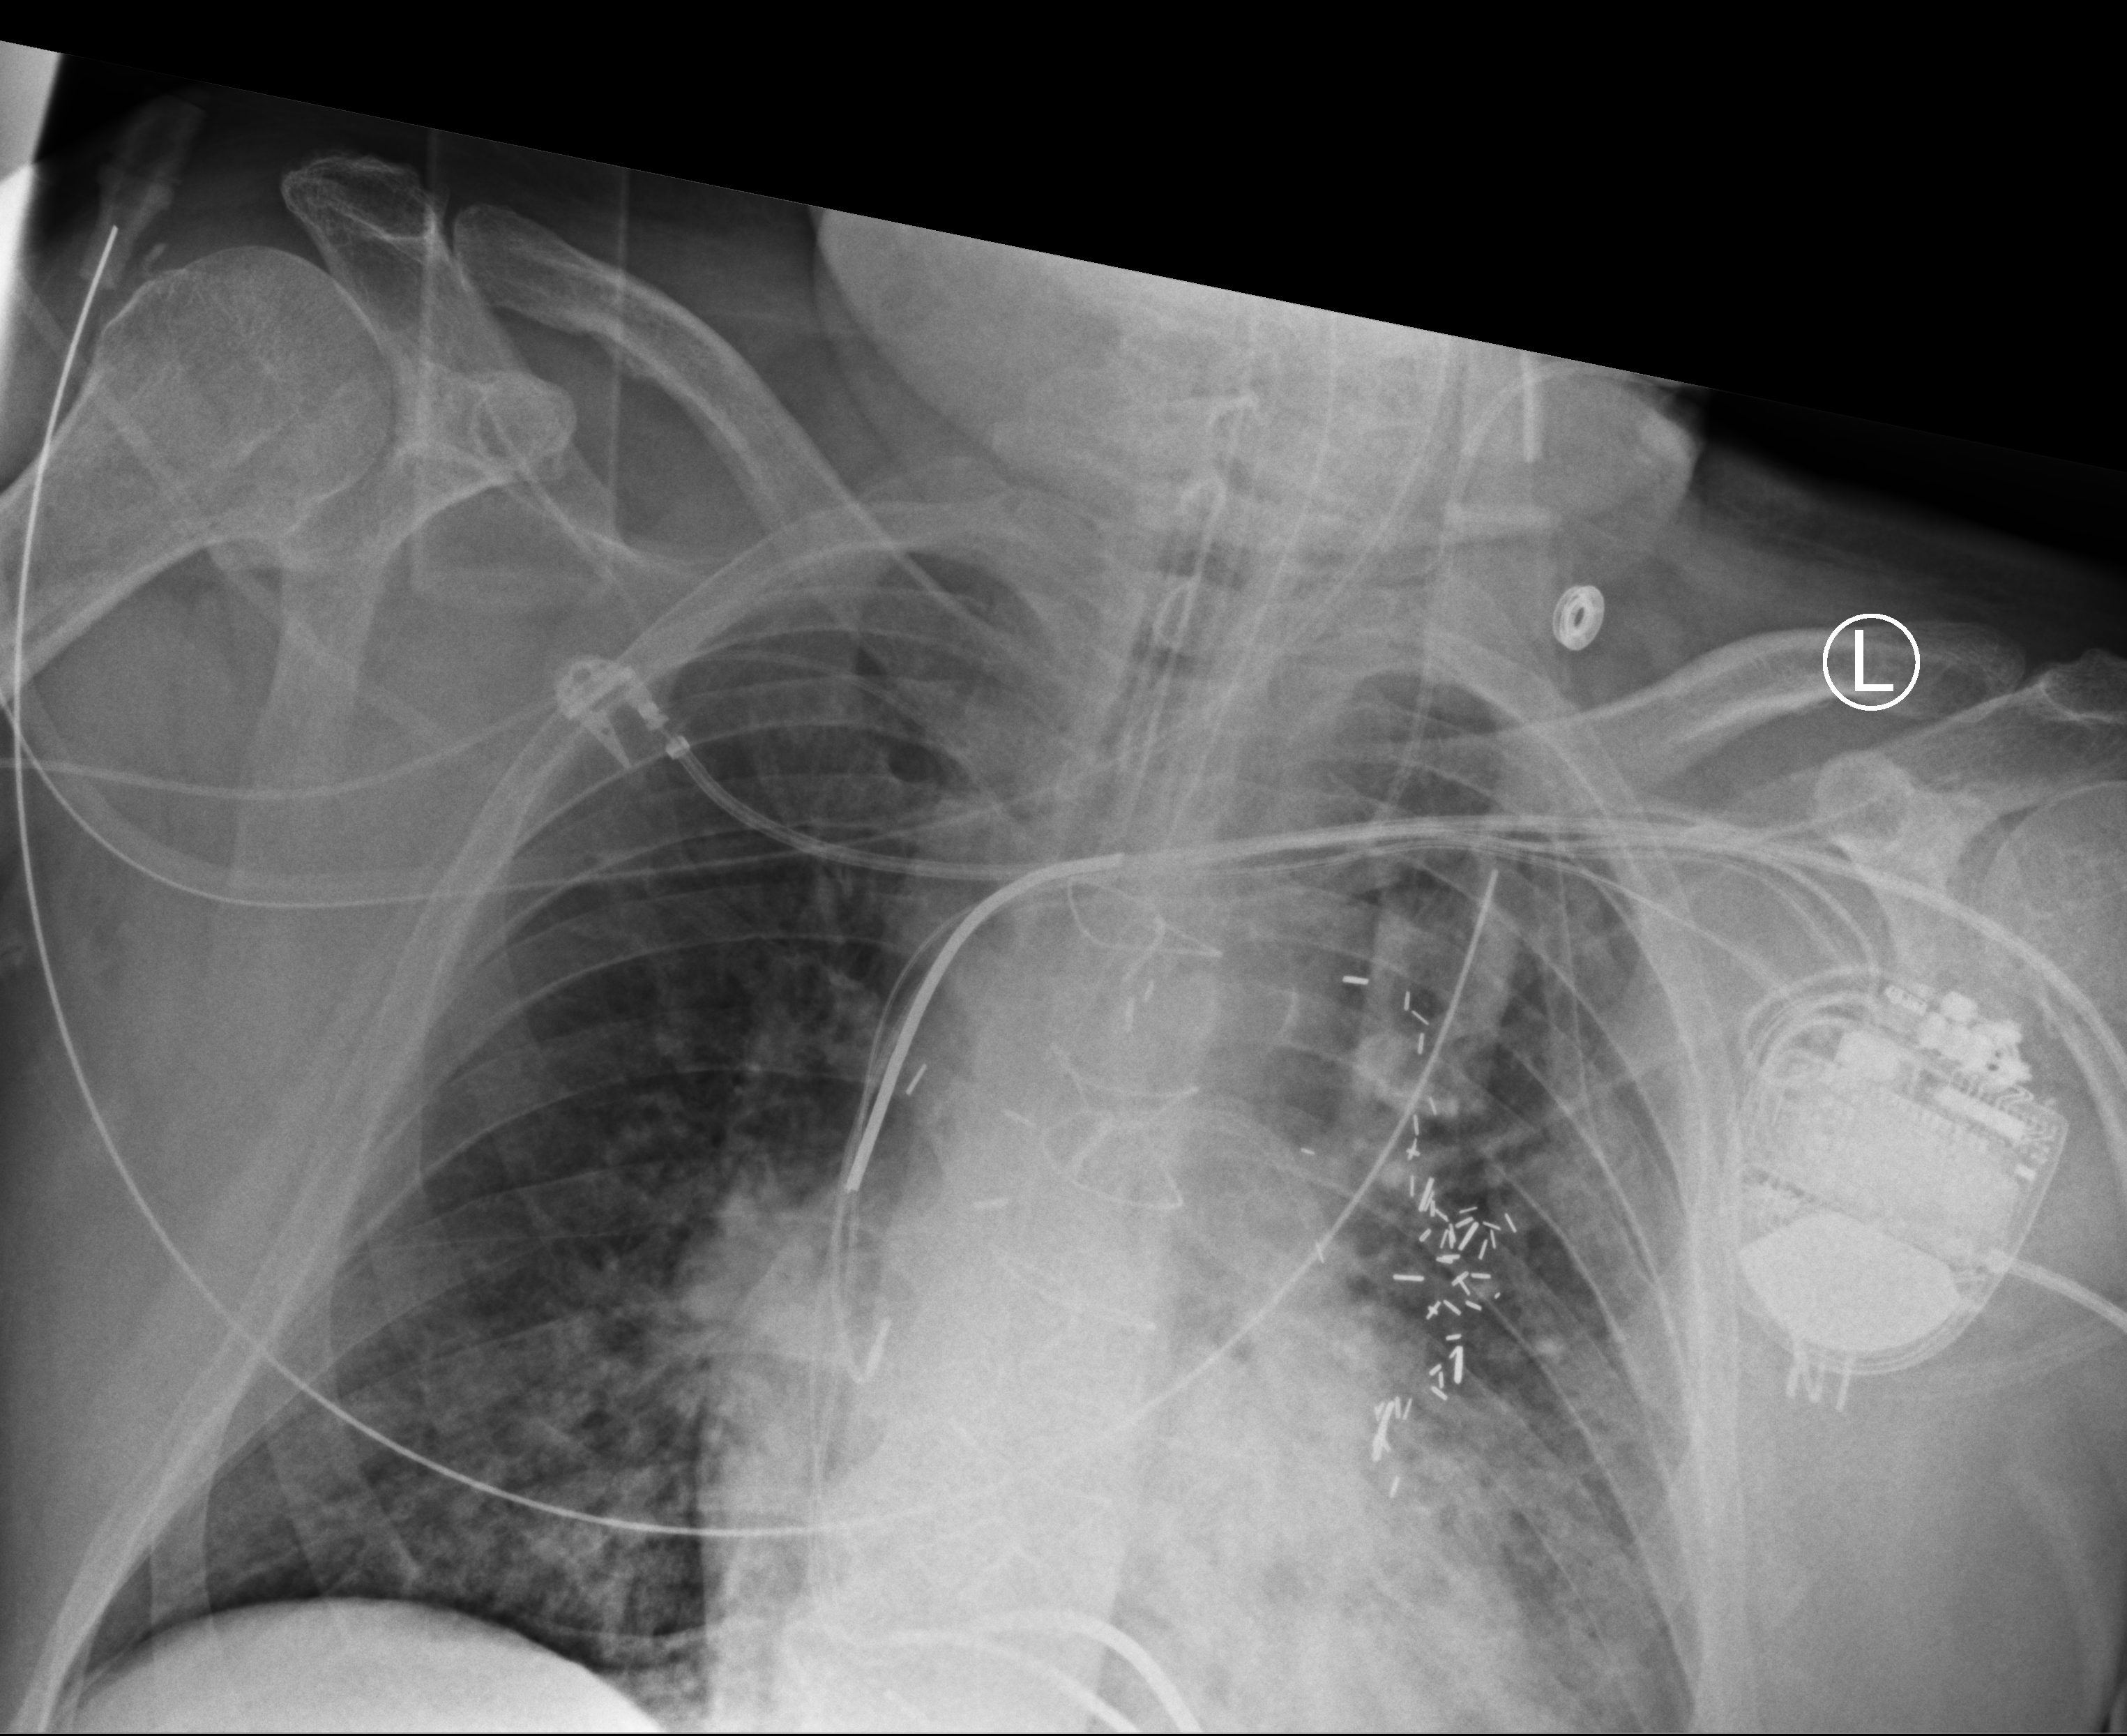
Bedside chest radiograph (computed radiography); anteroposterior (AP) projection. Male patient hospitalised with COVID-19, age 60–74 years.
Hospital-stay facts (about this admission, not read from this image; timing relative to this image not recorded):
- admitted to intensive care during this hospital stay: yes
- length of hospital stay: 55 days
- mechanically ventilated during this hospital stay: yes